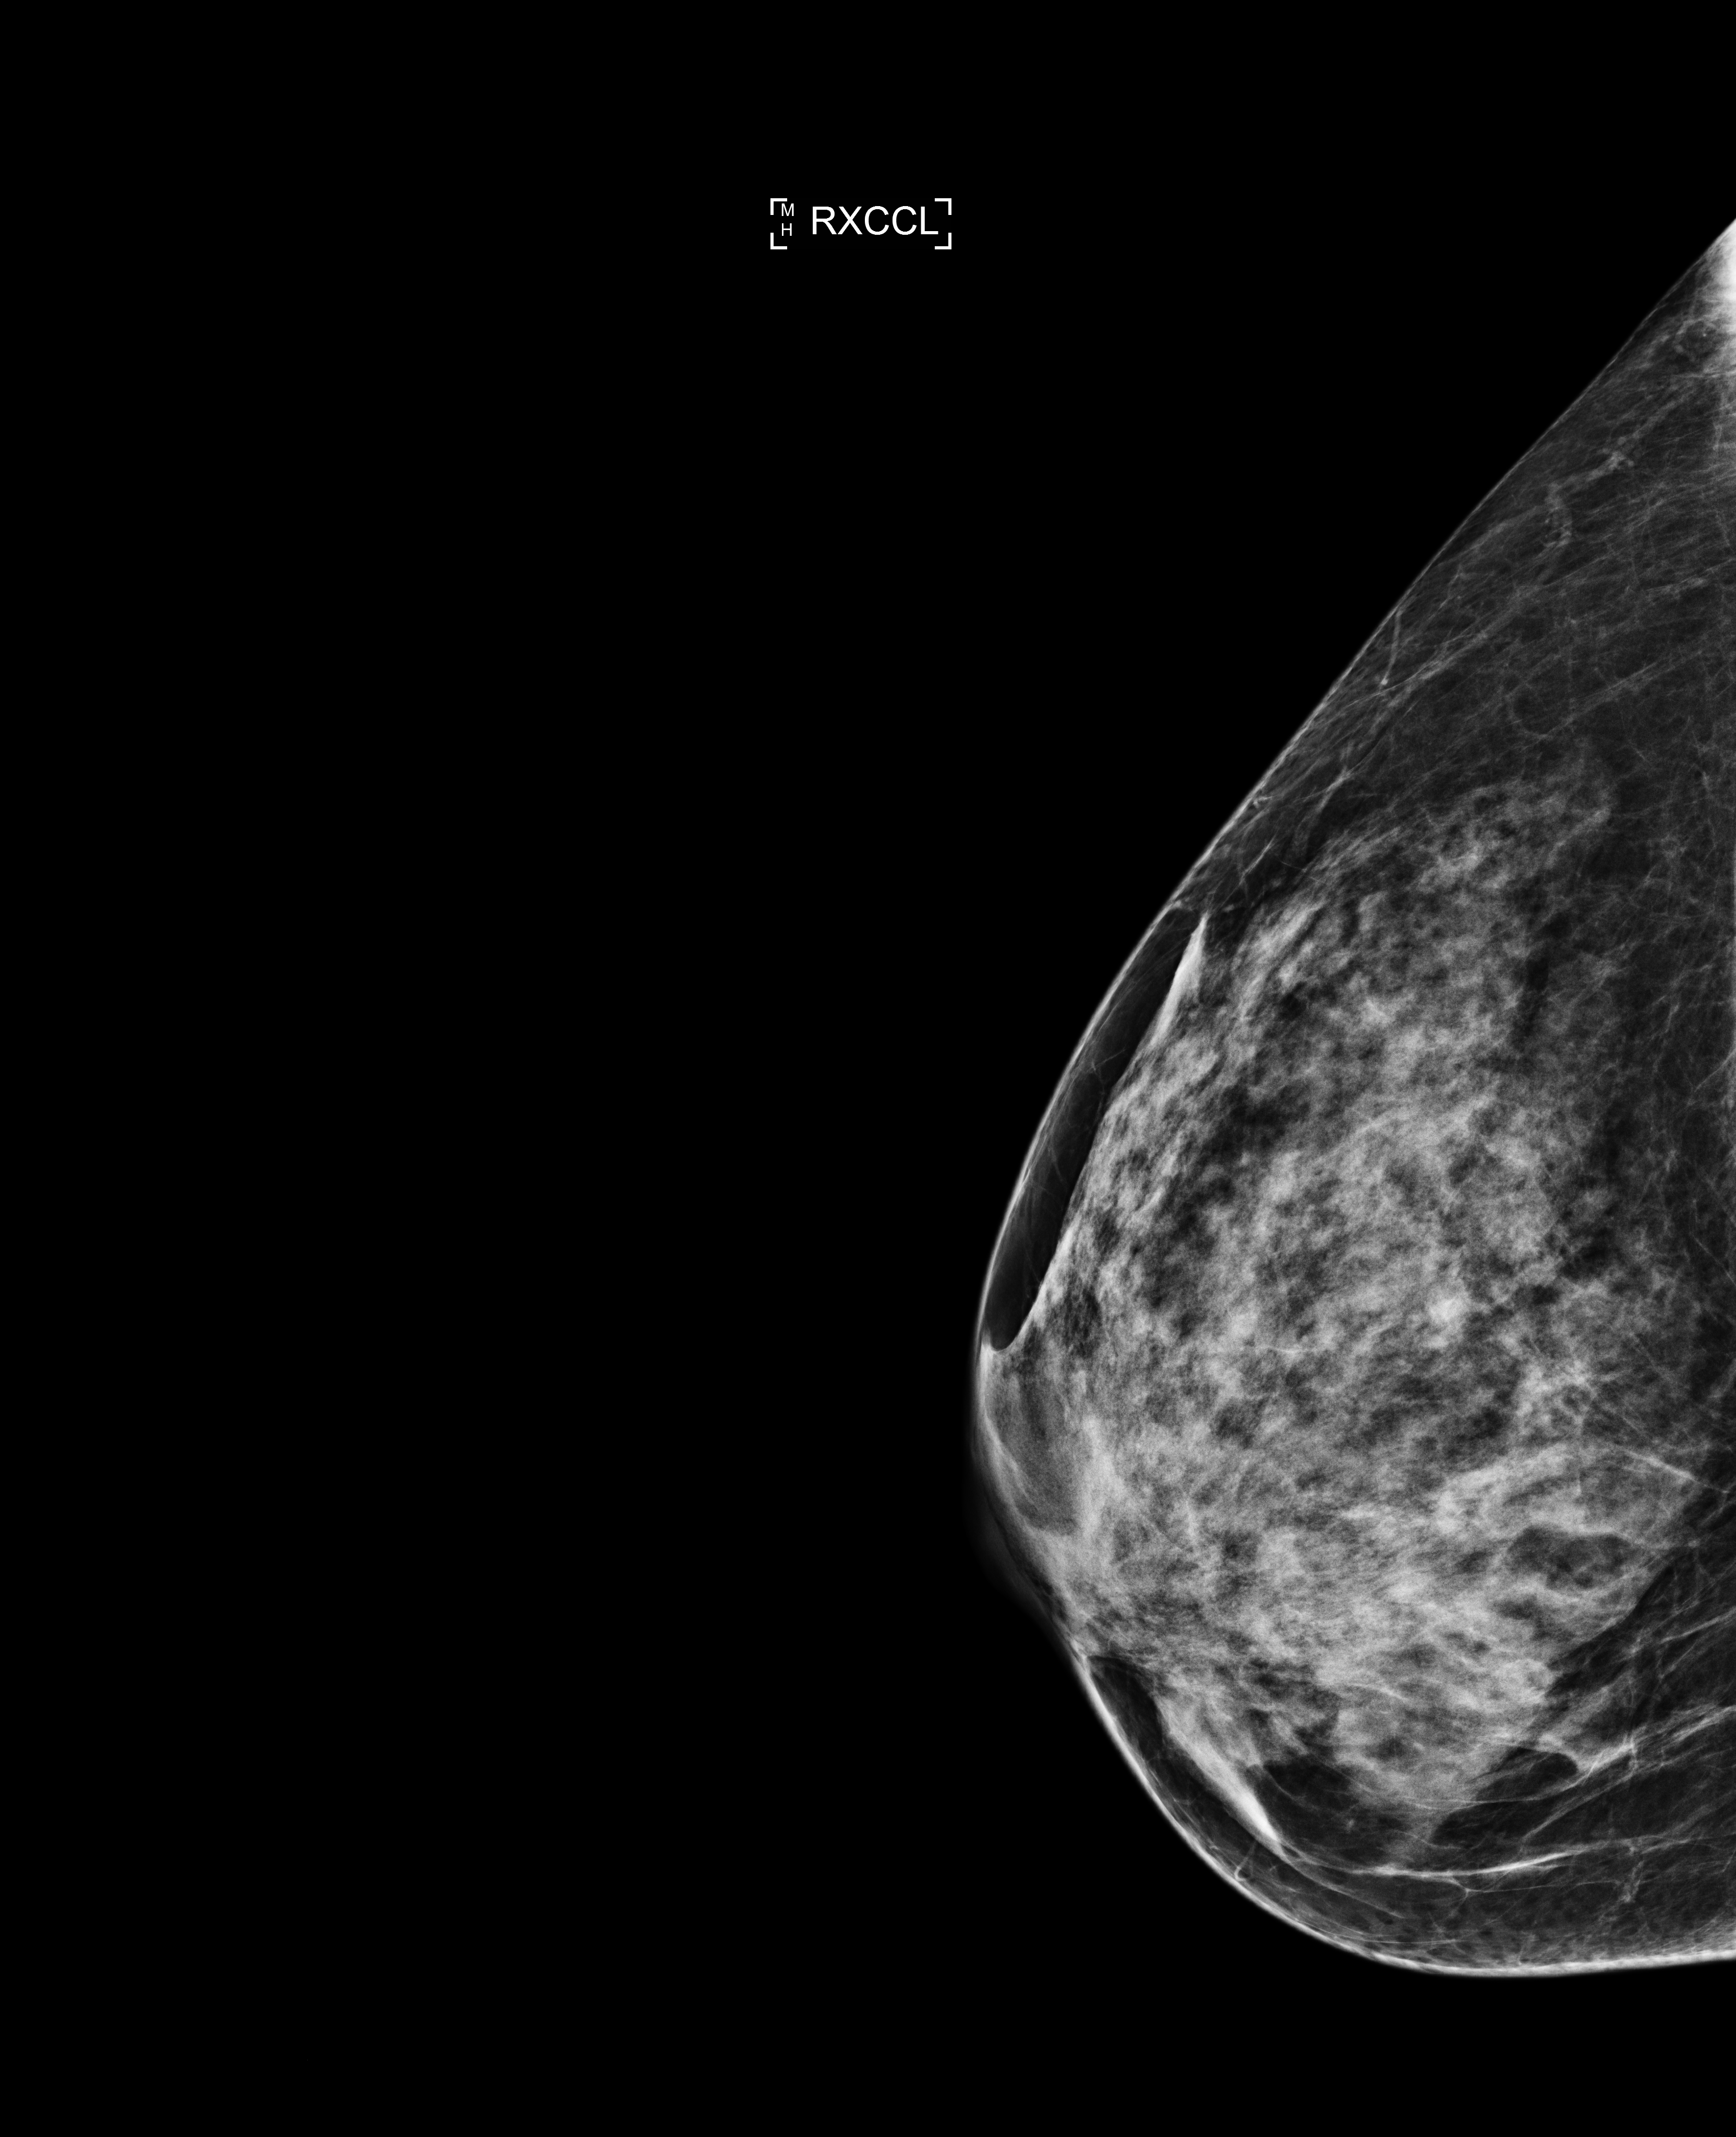
Full-field digital mammogram (FFDM), right breast, exaggerated CC view (lateral), annual screening mammography examination, compressed breast thickness 56 mm, system: Selenia Dimensions. Female patient, age 41 years.
- BI-RADS breast density category at the screening exam (both breasts, scale 1–4): 4
- final BI-RADS category for the screening round (tomosynthesis exam, both breasts): category 1
- recall: no recall after this screen